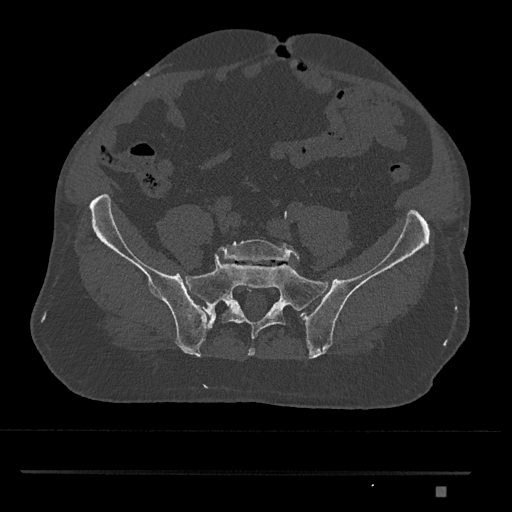
CT including the spine, one axial slice; position 509 of 1134 along the scan axis; reconstruction kernel Br40s/3; 120 kVp; bone window (W 1800 / L 400 HU); 0.5 mm slice thickness; 512 × 512 image matrix, field of view 429 × 429 mm. Patient: male, 65 years. From the clinical record (not read from this slice): primary cancer: prostate.
Annotated regions visible in this slice (semi-automatically segmented with operator editing):
- L5 vertebra: bounding box [x1, y1, x2, y2] px = [218, 239, 300, 264]